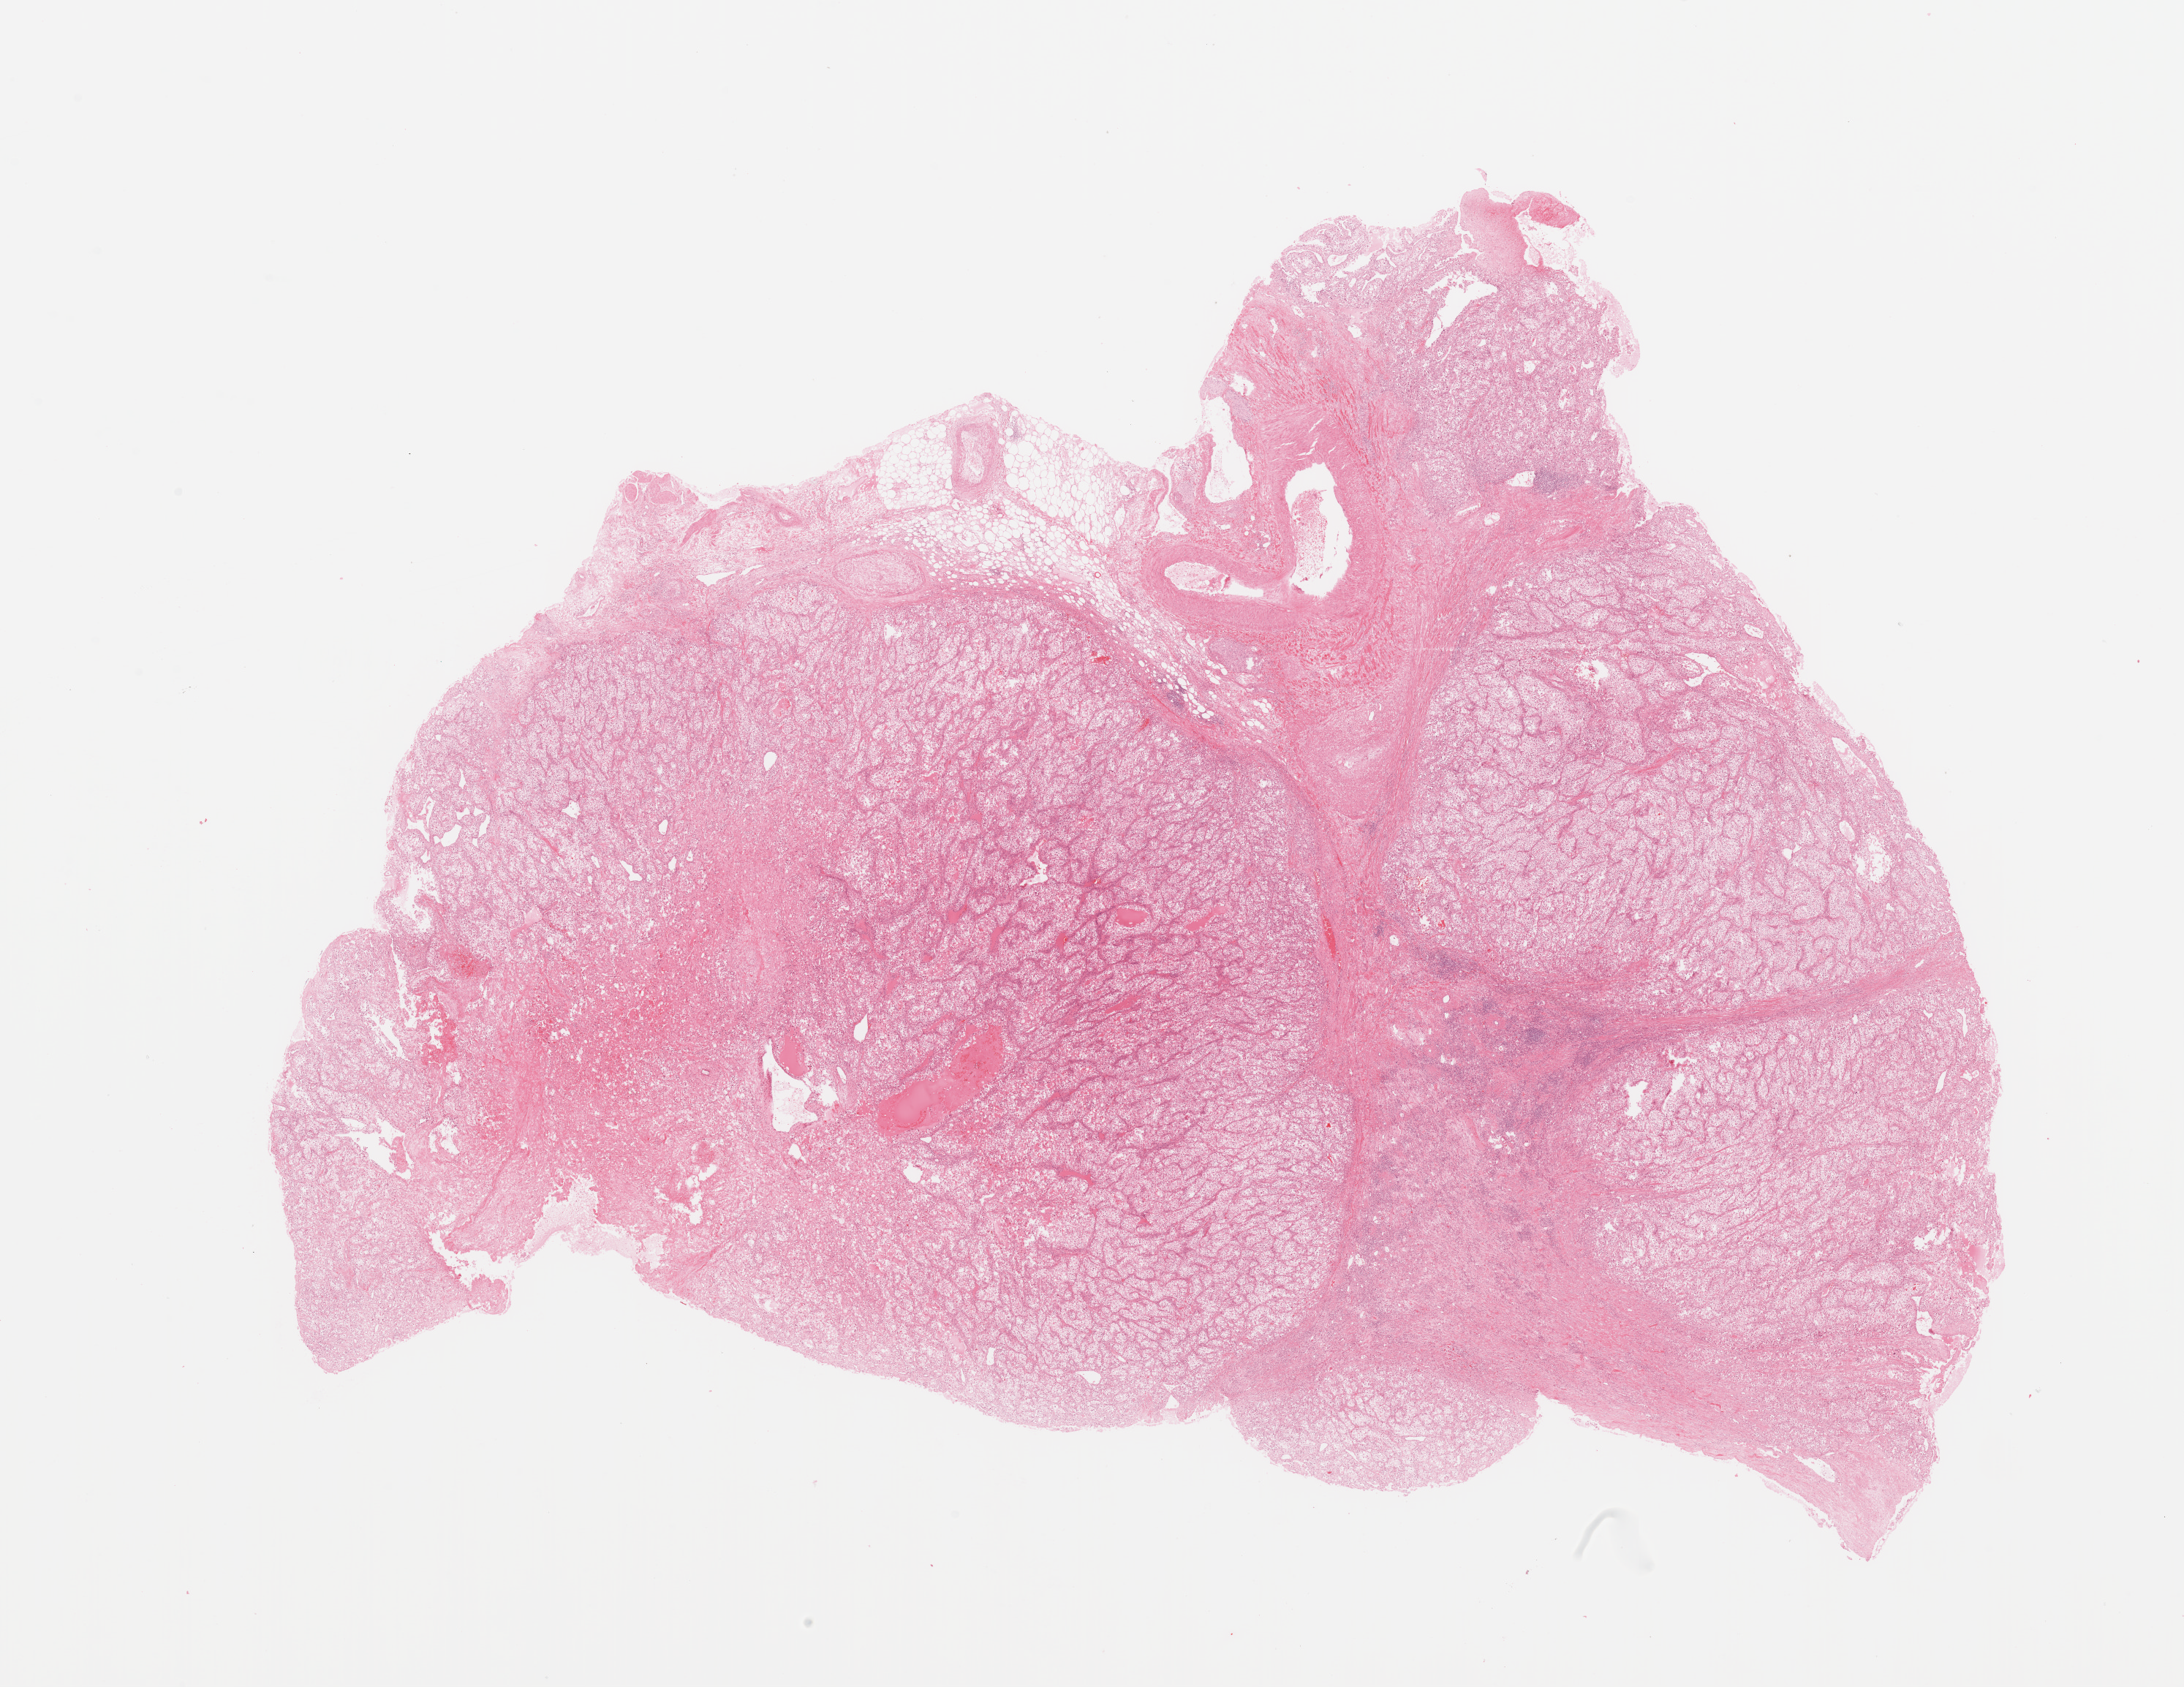
H&E whole-slide image — shown as a low-resolution overview of the whole scanned area (about 23.6 x 18.2 mm, acquisition: 20x scan); tumour tissue sample, kidney. 60-year-old male patient. Histologic grade: G3 (poorly differentiated).
Diagnosis: Renal cell carcinoma, NOS.